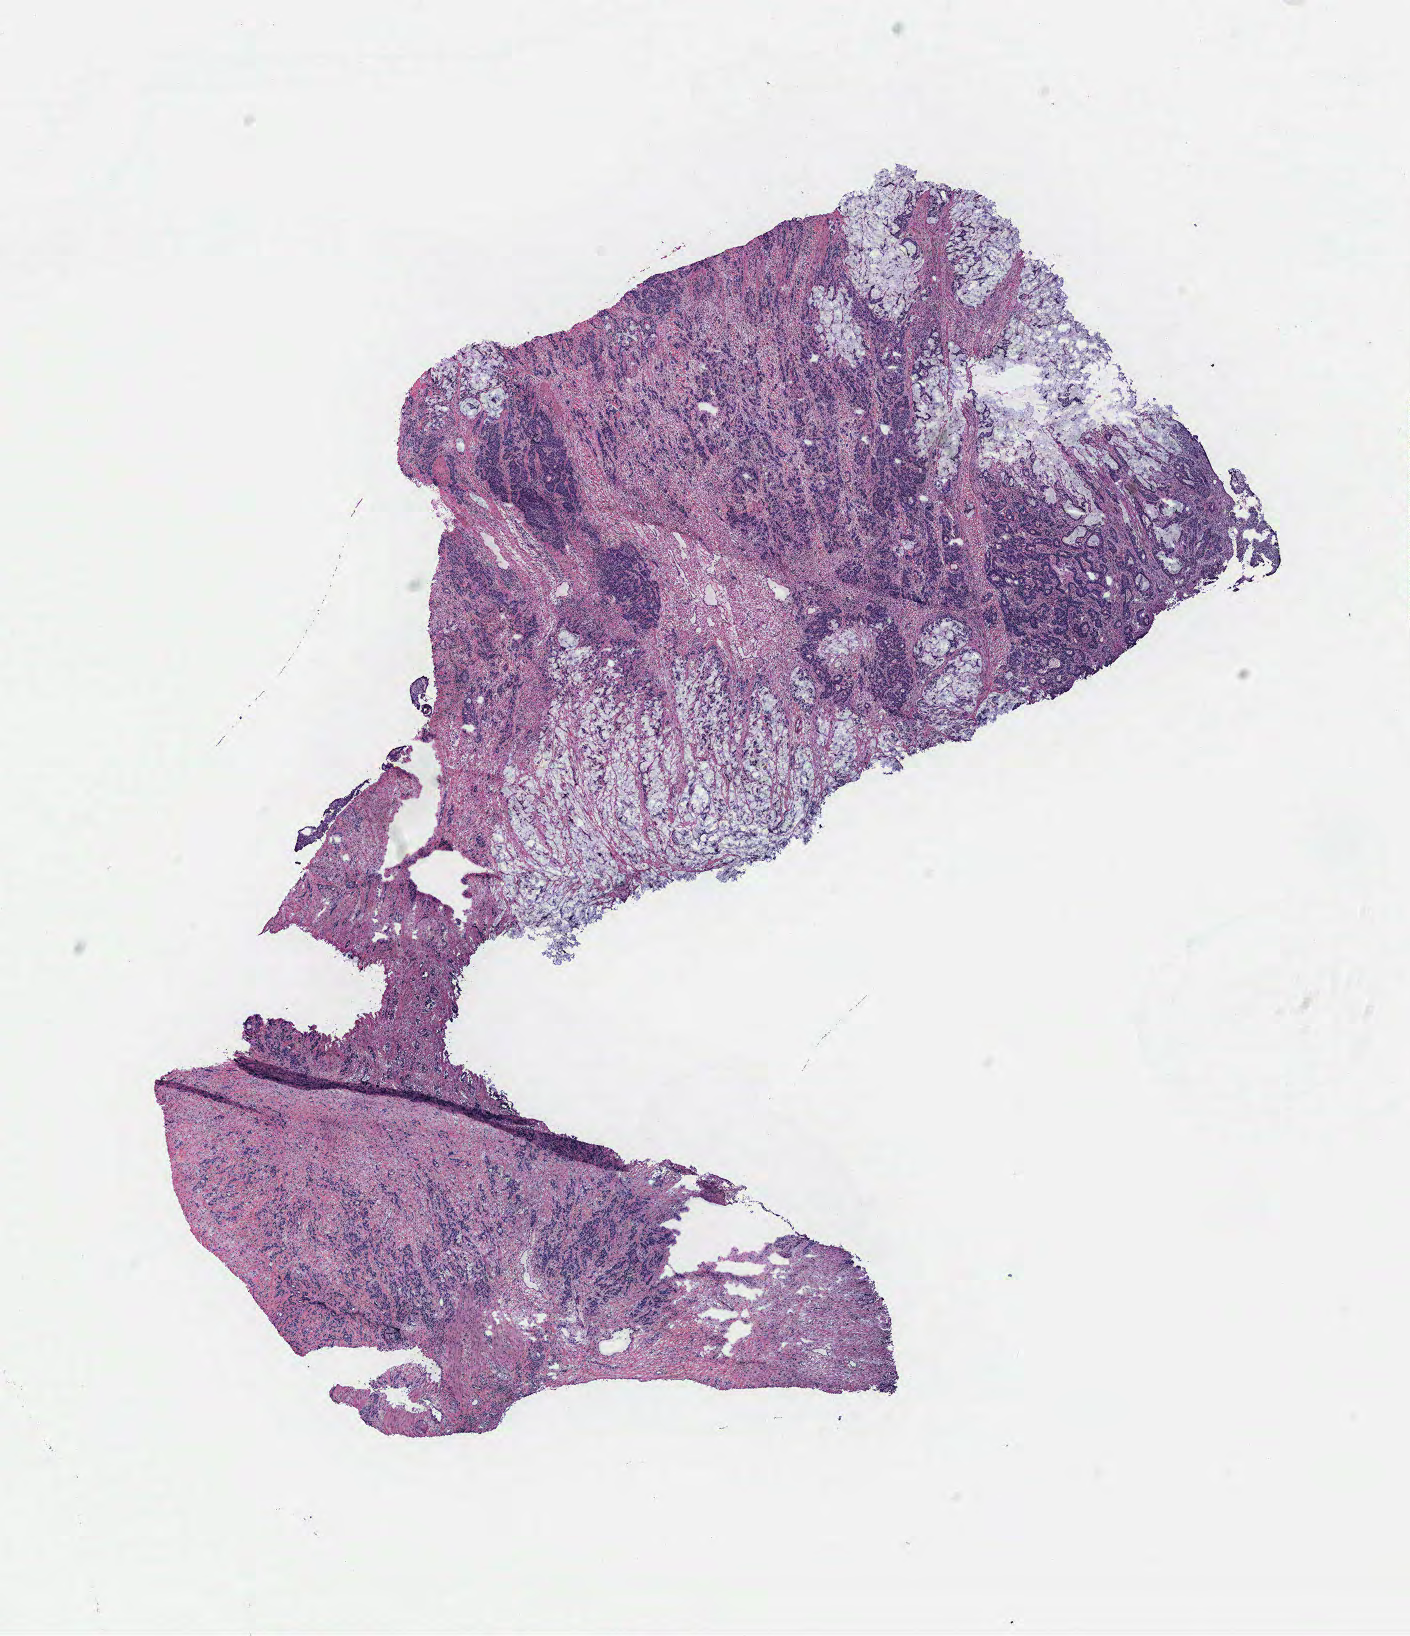
H&E whole-slide image, a low-resolution overview of the entire scanned area, about 11.3 x 13.1 mm (from a 40x scan). Colon, tumour tissue. Patient: female, age 60 years.
Diagnosis: Adenocarcinoma, NOS.